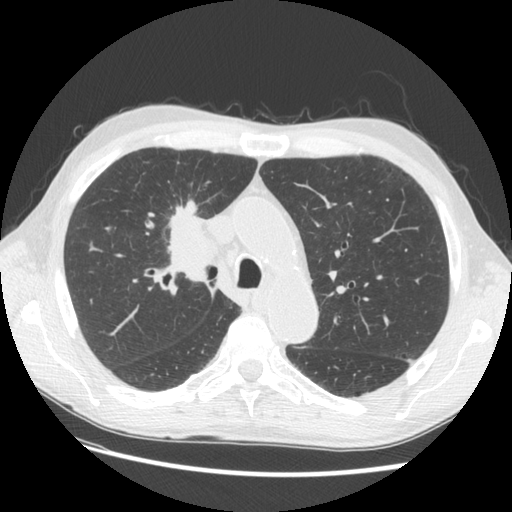
Low-dose screening chest CT, one axial slice; slice 94 of 133 in the series (ordered by position); lung window (W 1500 / L -600 HU); 2.5 mm slice thickness; 512 × 512 image matrix.
Outlined on this slice (outlined manually by an expert reader):
- lesion 1 (tumor, hilum of right lung): bounding box (x1, y1, x2, y2) in pixels: (168, 201, 216, 279)